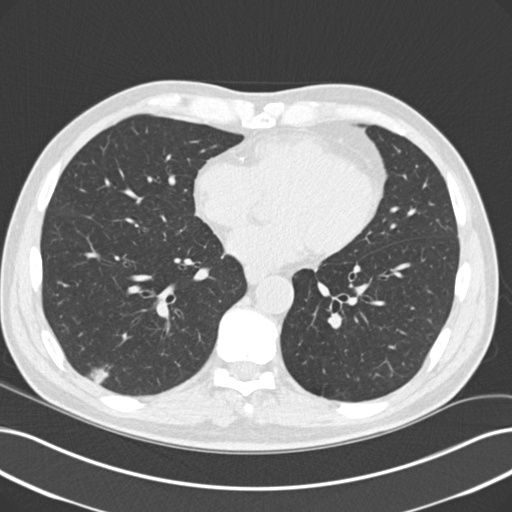
Low-dose screening chest CT, axial slice. Baseline screening round. Lung window (W 1500 / L -600 HU). 2 mm slice thickness. 120 kVp. 512 × 512 image matrix, field of view 366 × 366 mm. Male participant, aged 60 years at enrolment.
• Lesion marked by an expert reader, bounding box (x1, y1, x2, y2) in pixels: (75, 357, 120, 402).
• The screening reader recorded 2 non-calcified nodules or masses ≥4 mm on this exam; which of them this box marks is not recorded.
• Official screen result: positive, change unspecified: nodule(s) >= 4 mm or enlarging nodule(s), mass(es), or other non-specific abnormalities suspicious for lung cancer.
• Participant outcome: lung cancer diagnosed 64 days after this screen — acinar cell carcinoma, right lower lobe, moderately differentiated (G2), stage IA (AJCC 6th edition), 16 mm at pathology.